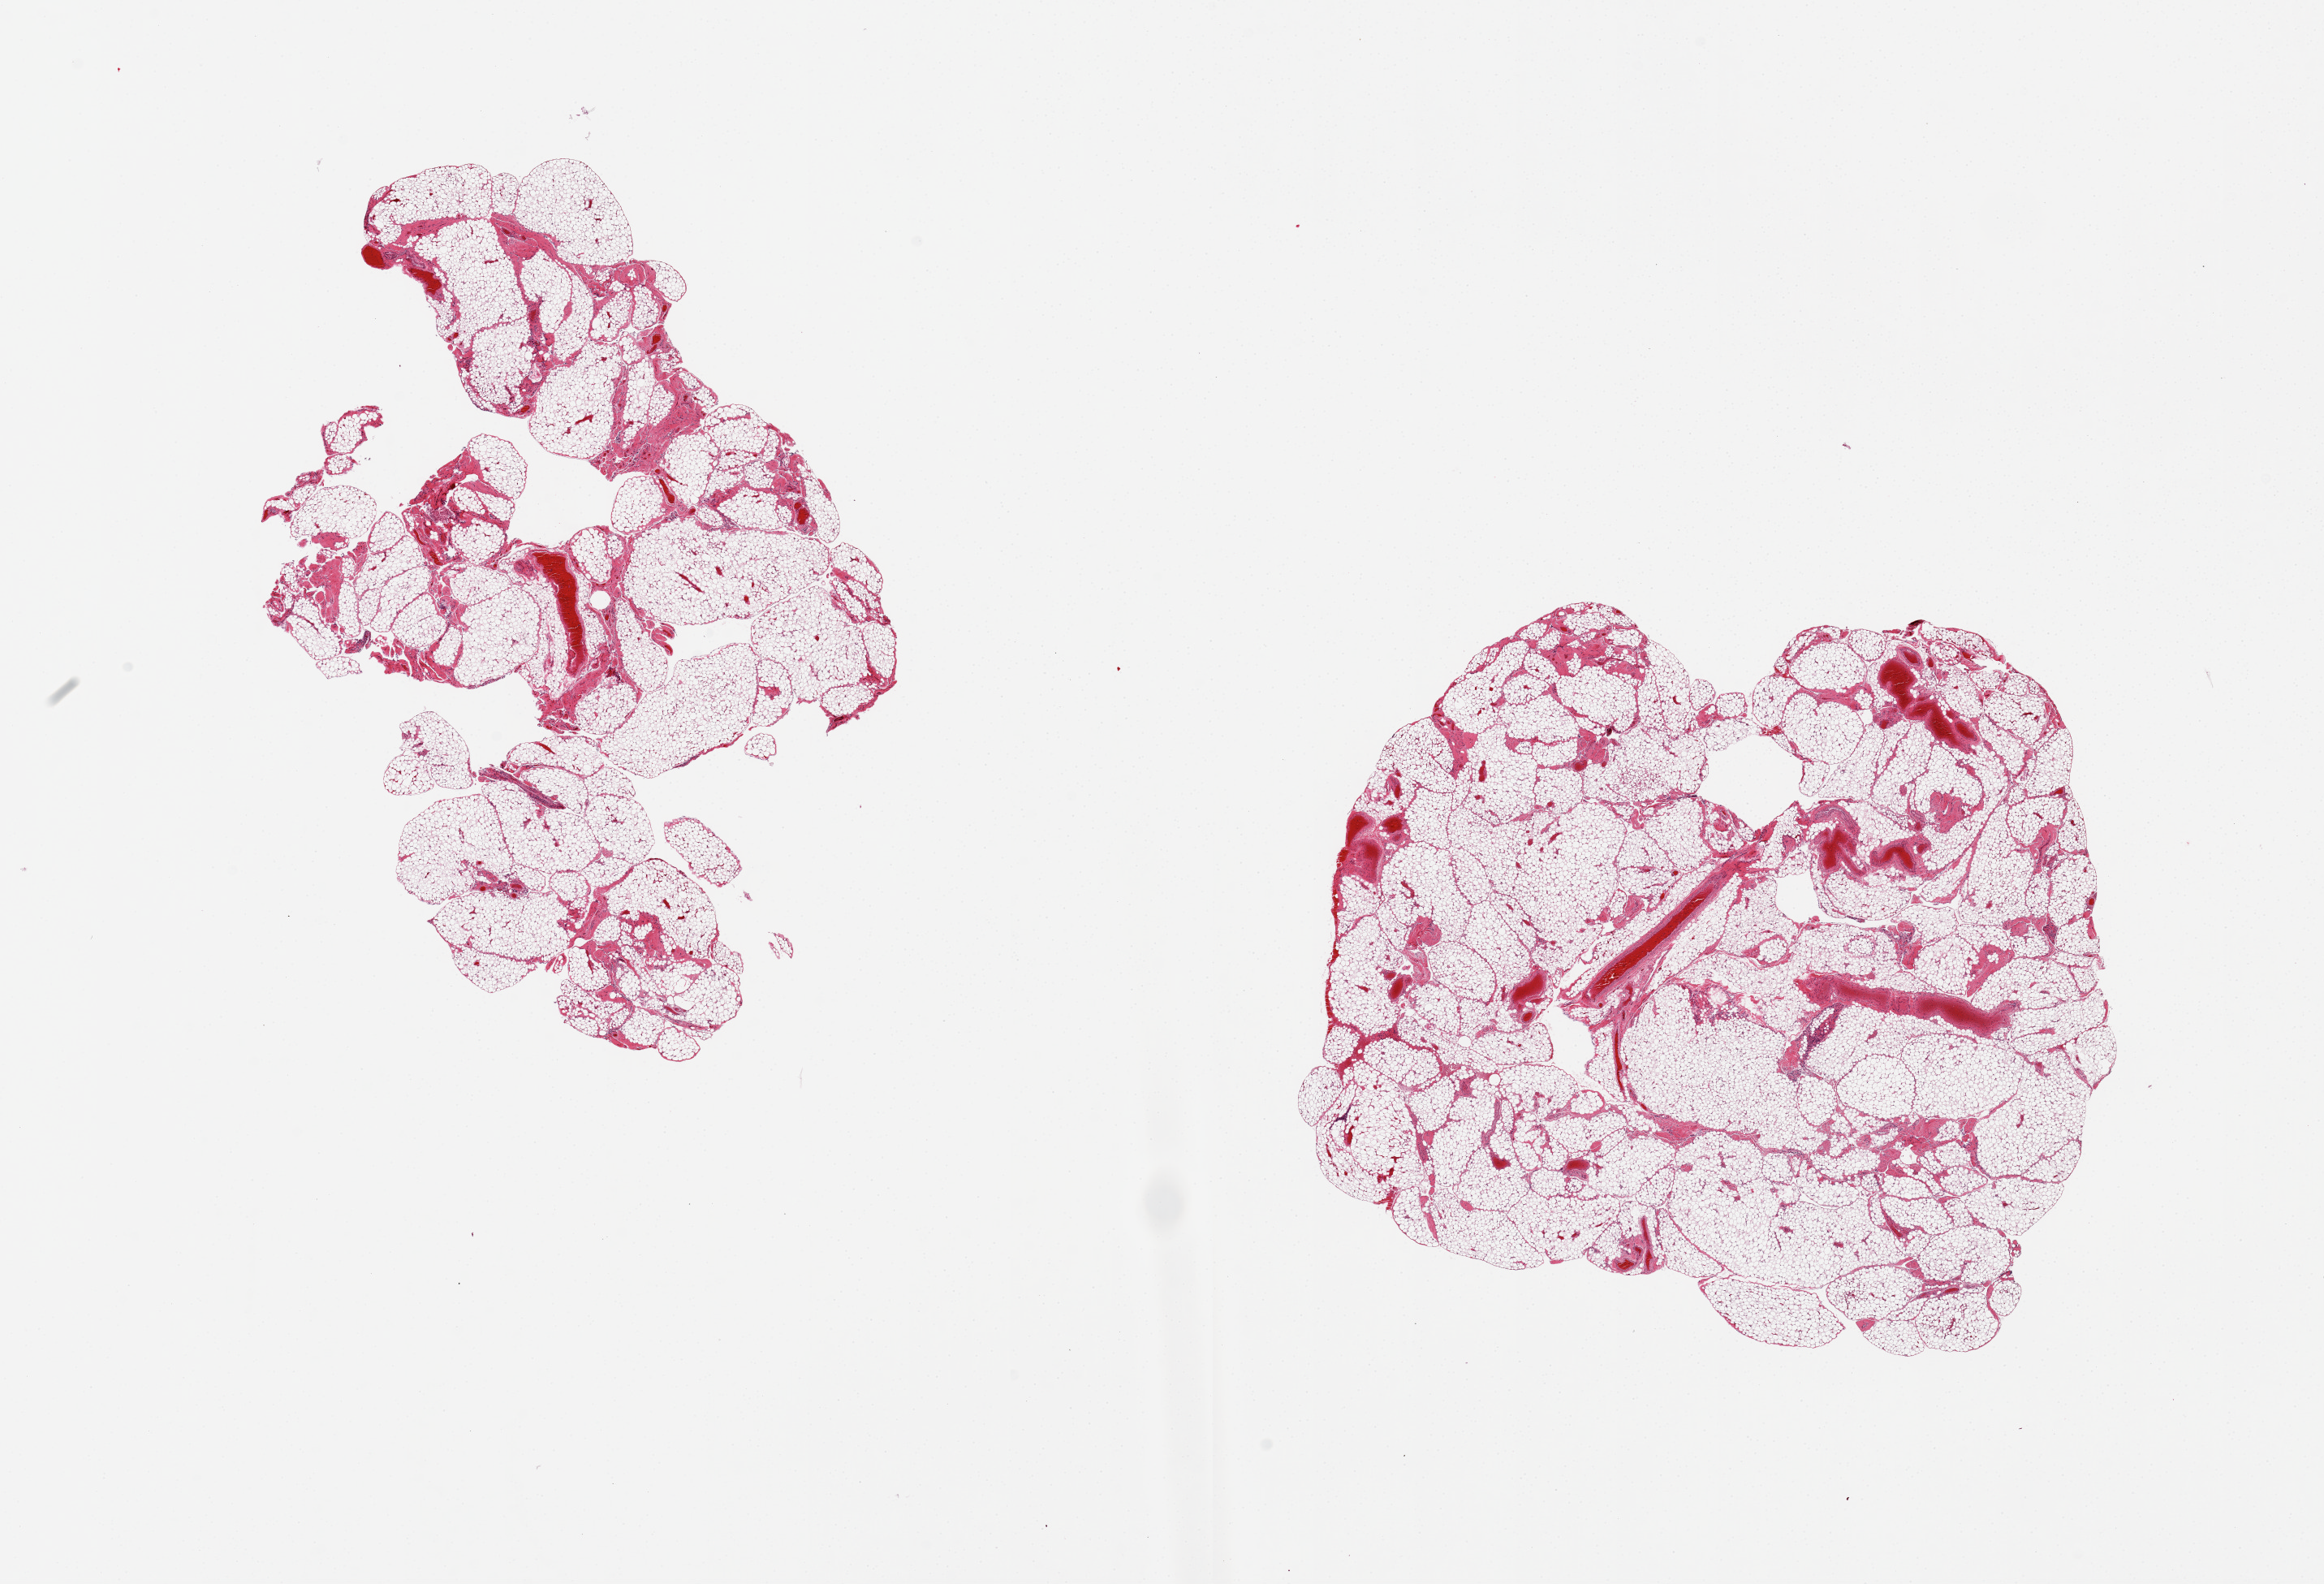
Haematoxylin and eosin whole-slide image, brightfield, whole scanned area (about 22.6 x 15.4 mm, from a 20x scan) shown as a low-resolution overview, PAXgene-fixed paraffin-embedded (PFPE) section, target tissue: omentum, donor tissue sample. Donor: female.
* reviewer comment on this tissue sample: 2 pieces, numerous prominent congested/engorged vessels